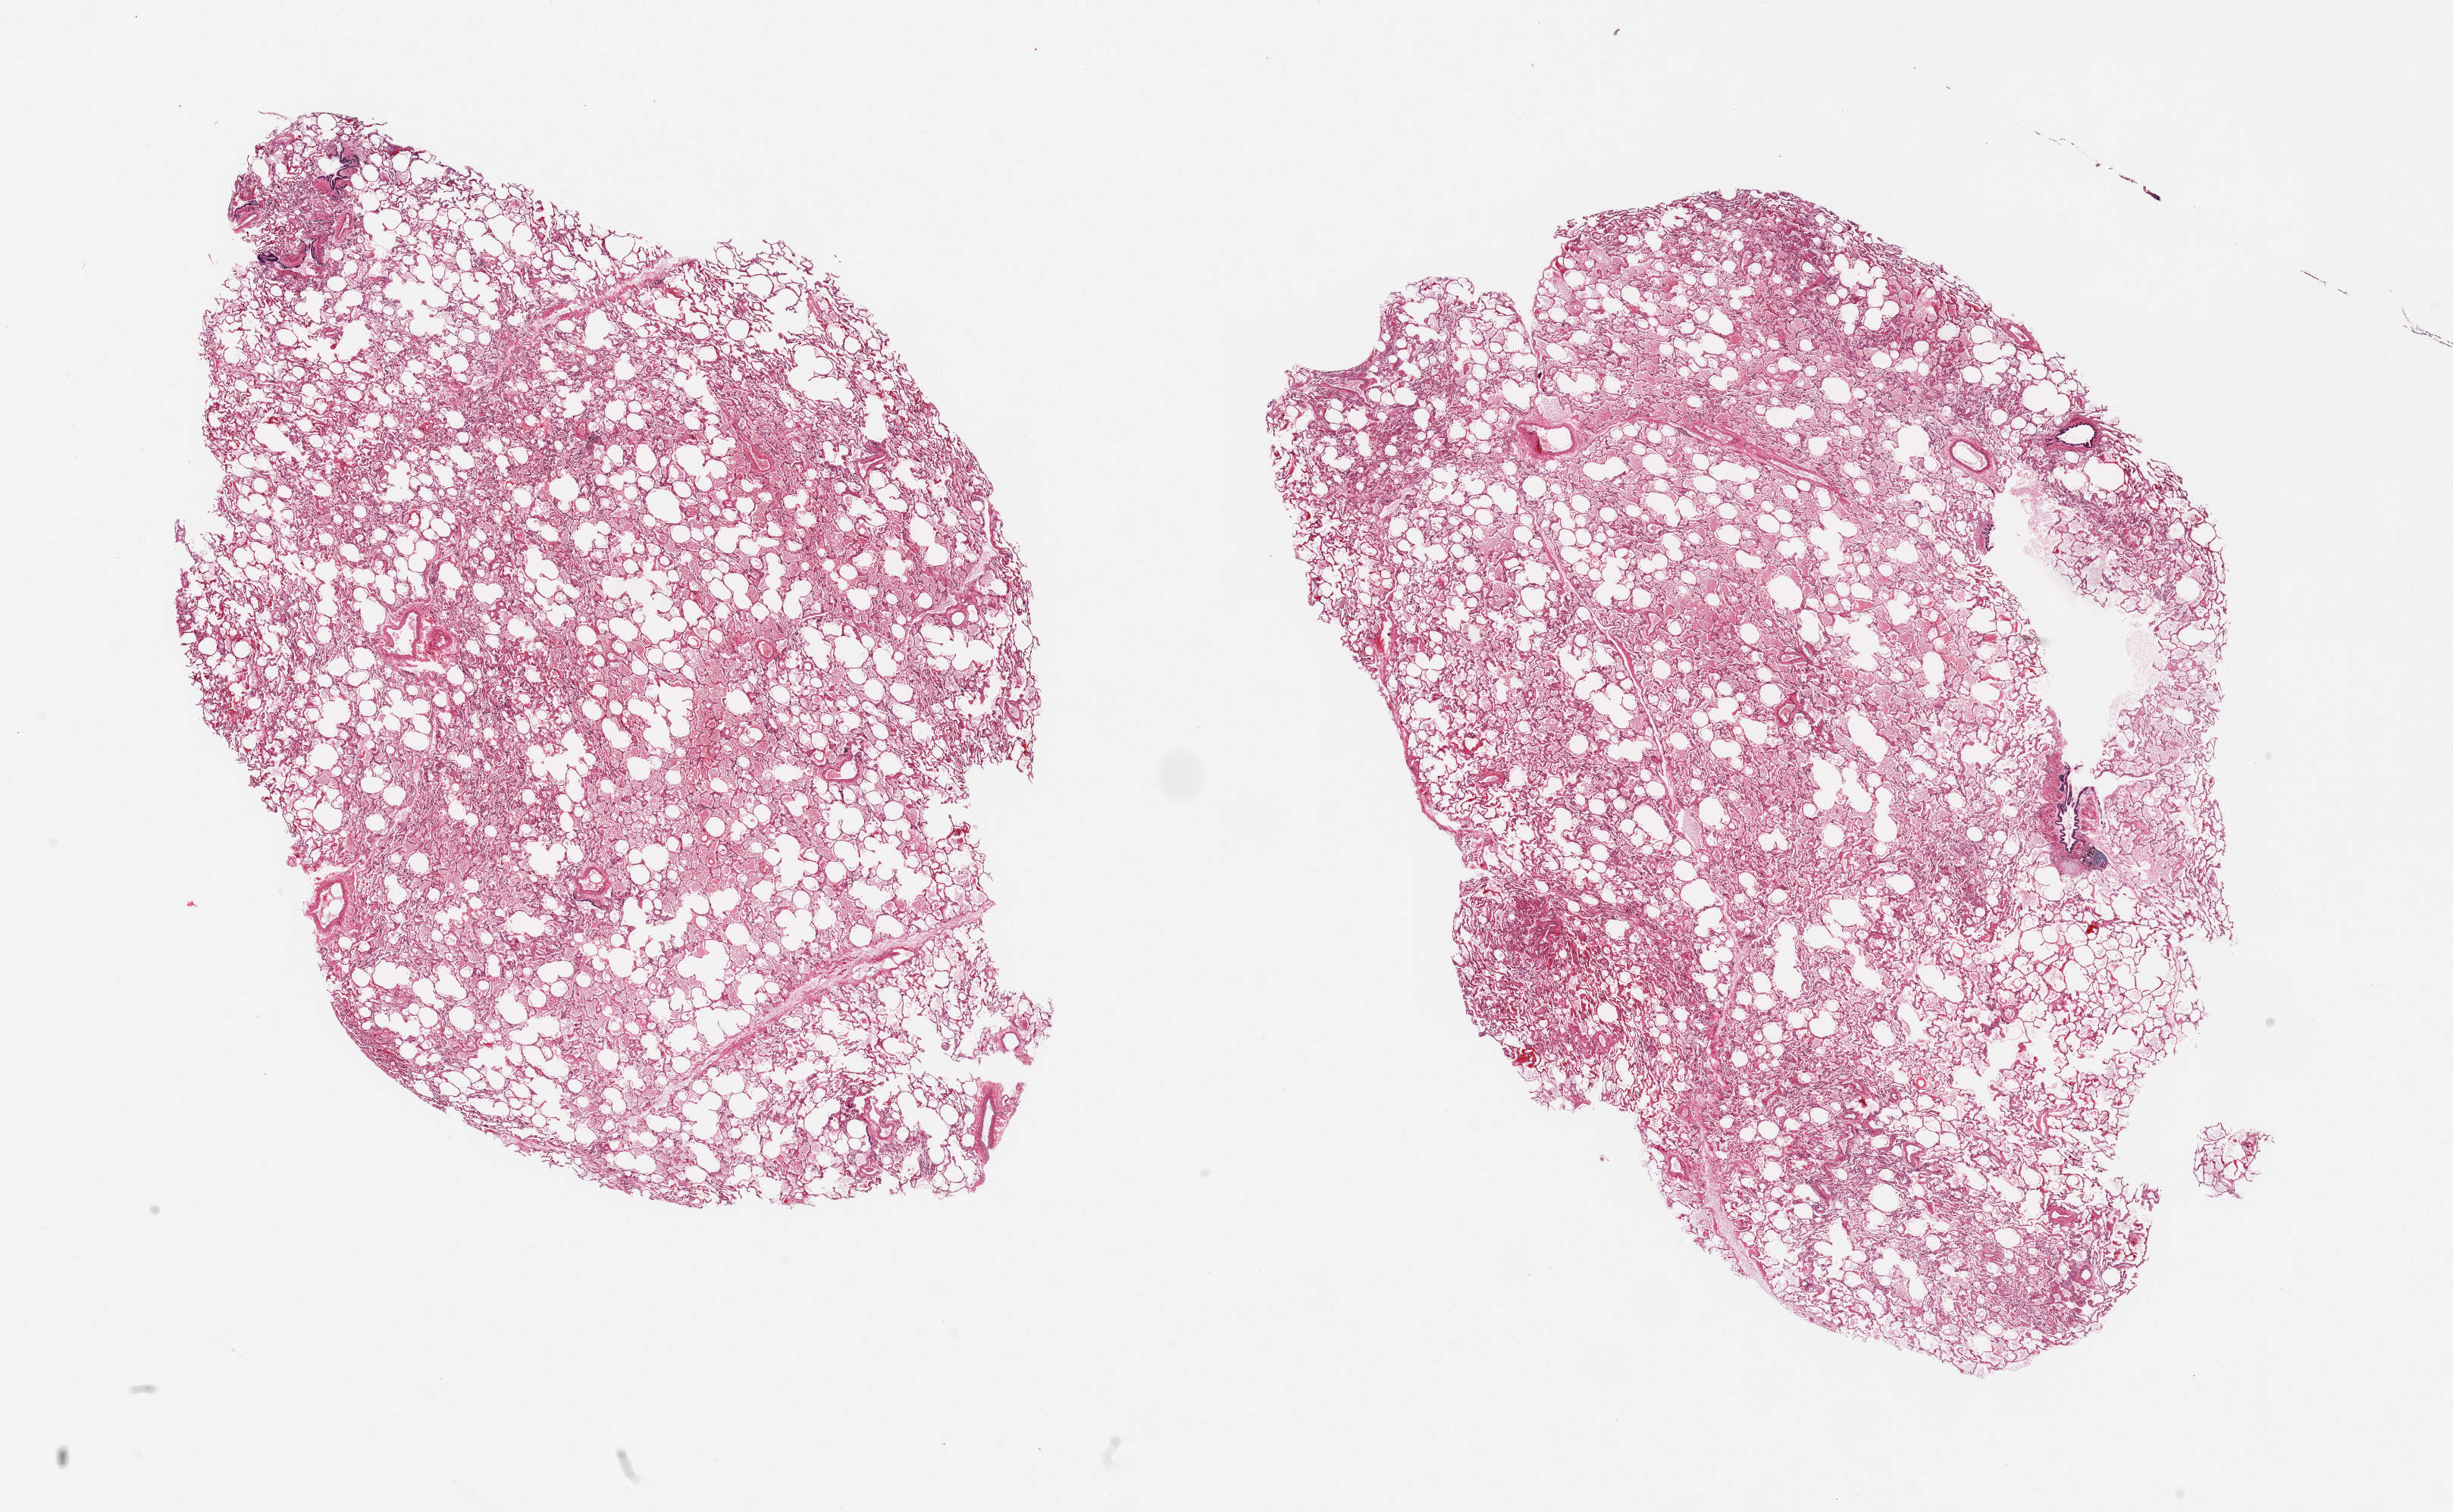
Whole-slide image, H&E stain — a low-resolution overview of the entire scanned area, about 25.6 x 15.8 mm (from a 20x scan), PAXgene-fixed, paraffin-embedded tissue, target tissue: lung, donor tissue sample.
Review note (as recorded): 2 pieces, moderate congestion/alveolar edema.